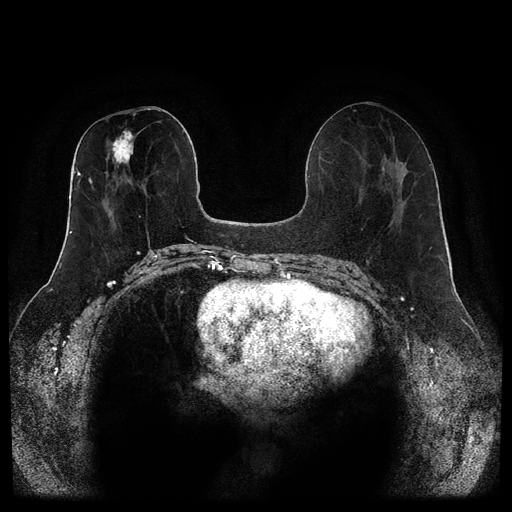
Breast MRI (dynamic contrast-enhanced, multi-phase), one axial slice. Position 47 of 116 along the scan axis. Dynamic contrast-enhanced series, time point 2 of 5 at this slice position (early post-contrast). 1.5 T. TE 2.6 ms, TR 5.3 ms. 512 × 512 image matrix, field of view 350 × 350 mm. Female patient, age 46 years.
Annotated regions visible in this slice (semi-automatically segmented with operator editing):
- breast lesion (labelled 'tumour' in the annotation; benign lesions carry a separate 'benign' label): bounding box <111,129,135,167> (left, top, right, bottom; pixels)